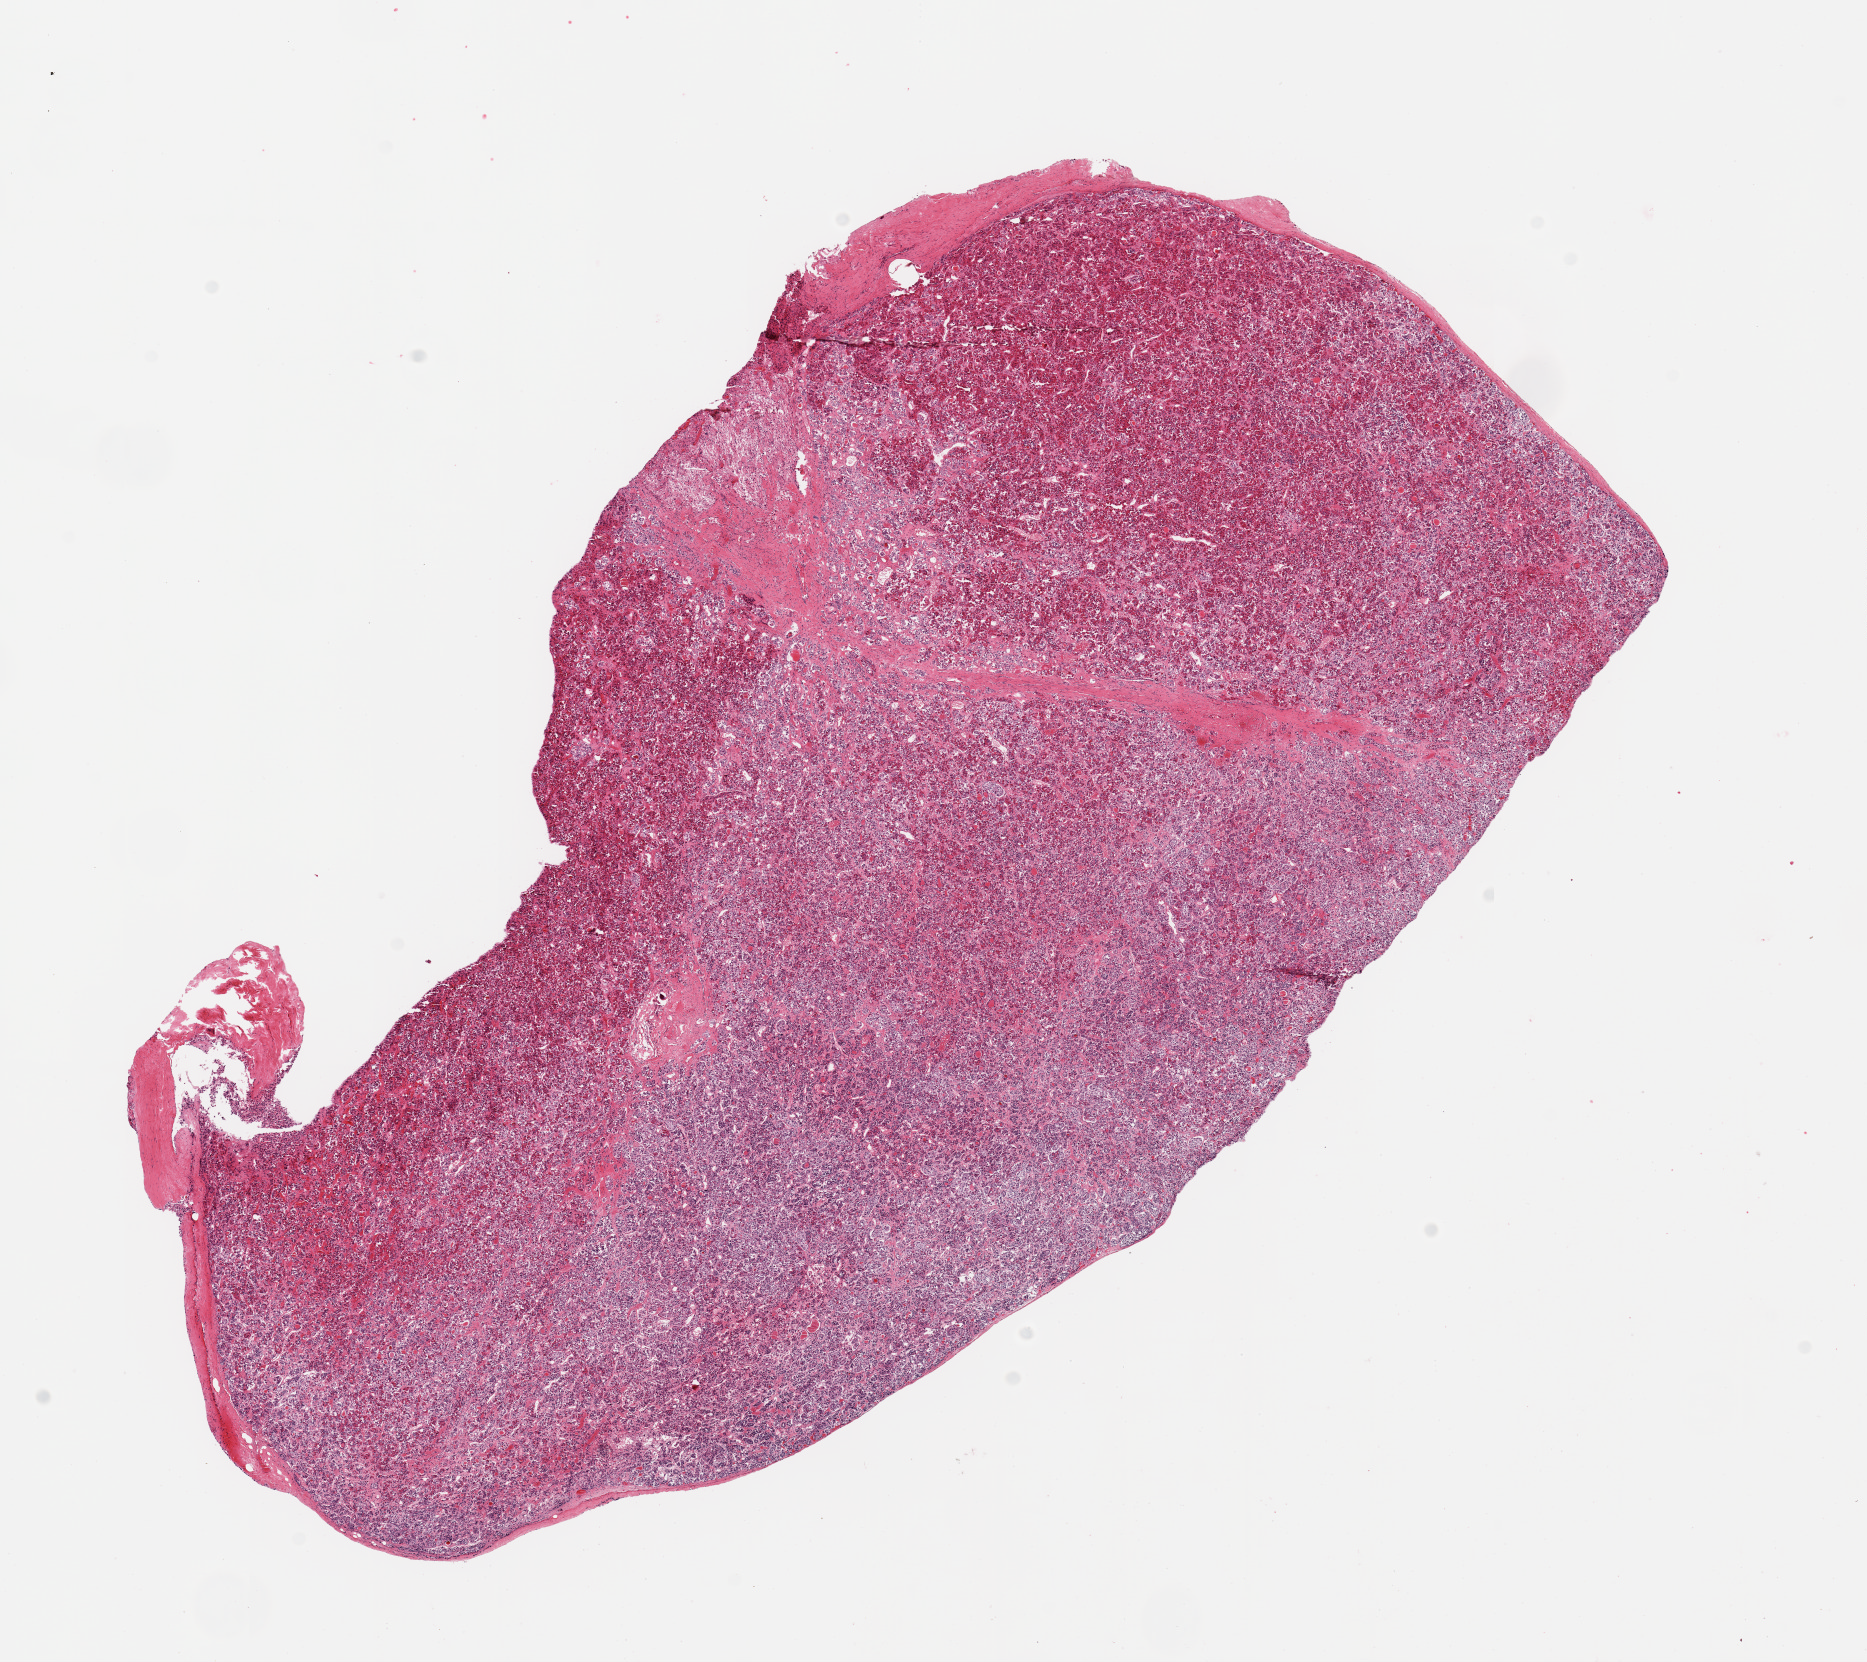
Haematoxylin and eosin whole-slide image, shown as a low-resolution overview of the whole scanned area (about 14.8 x 13.1 mm). PAXgene-fixed, paraffin-embedded tissue. Section of pituitary (target tissue). Donor tissue sample. Donor sex: male.
* reviewer comment on this tissue sample: 1 piece